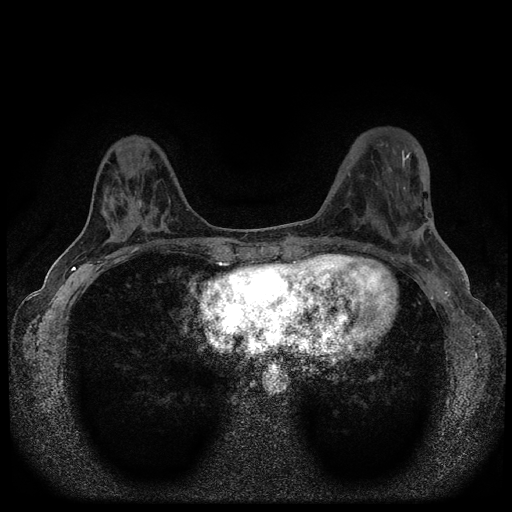
Breast MRI (dynamic contrast-enhanced, multi-phase), one axial slice; slice 38 of 116 in the series (ordered by position); dynamic contrast-enhanced series, time point 2 of 5 at this slice position (early post-contrast); 1.5 T; TE 2.7 ms, TR 5.6 ms; 2 mm slice thickness; 512 × 512 image matrix, field of view 310 × 310 mm. Patient: female, 40 years.
Annotated regions visible in this slice (semi-automatically segmented with operator editing):
- breast lesion (labelled benign in the annotation): bounding box <132,188,144,211> (left, top, right, bottom; pixels)